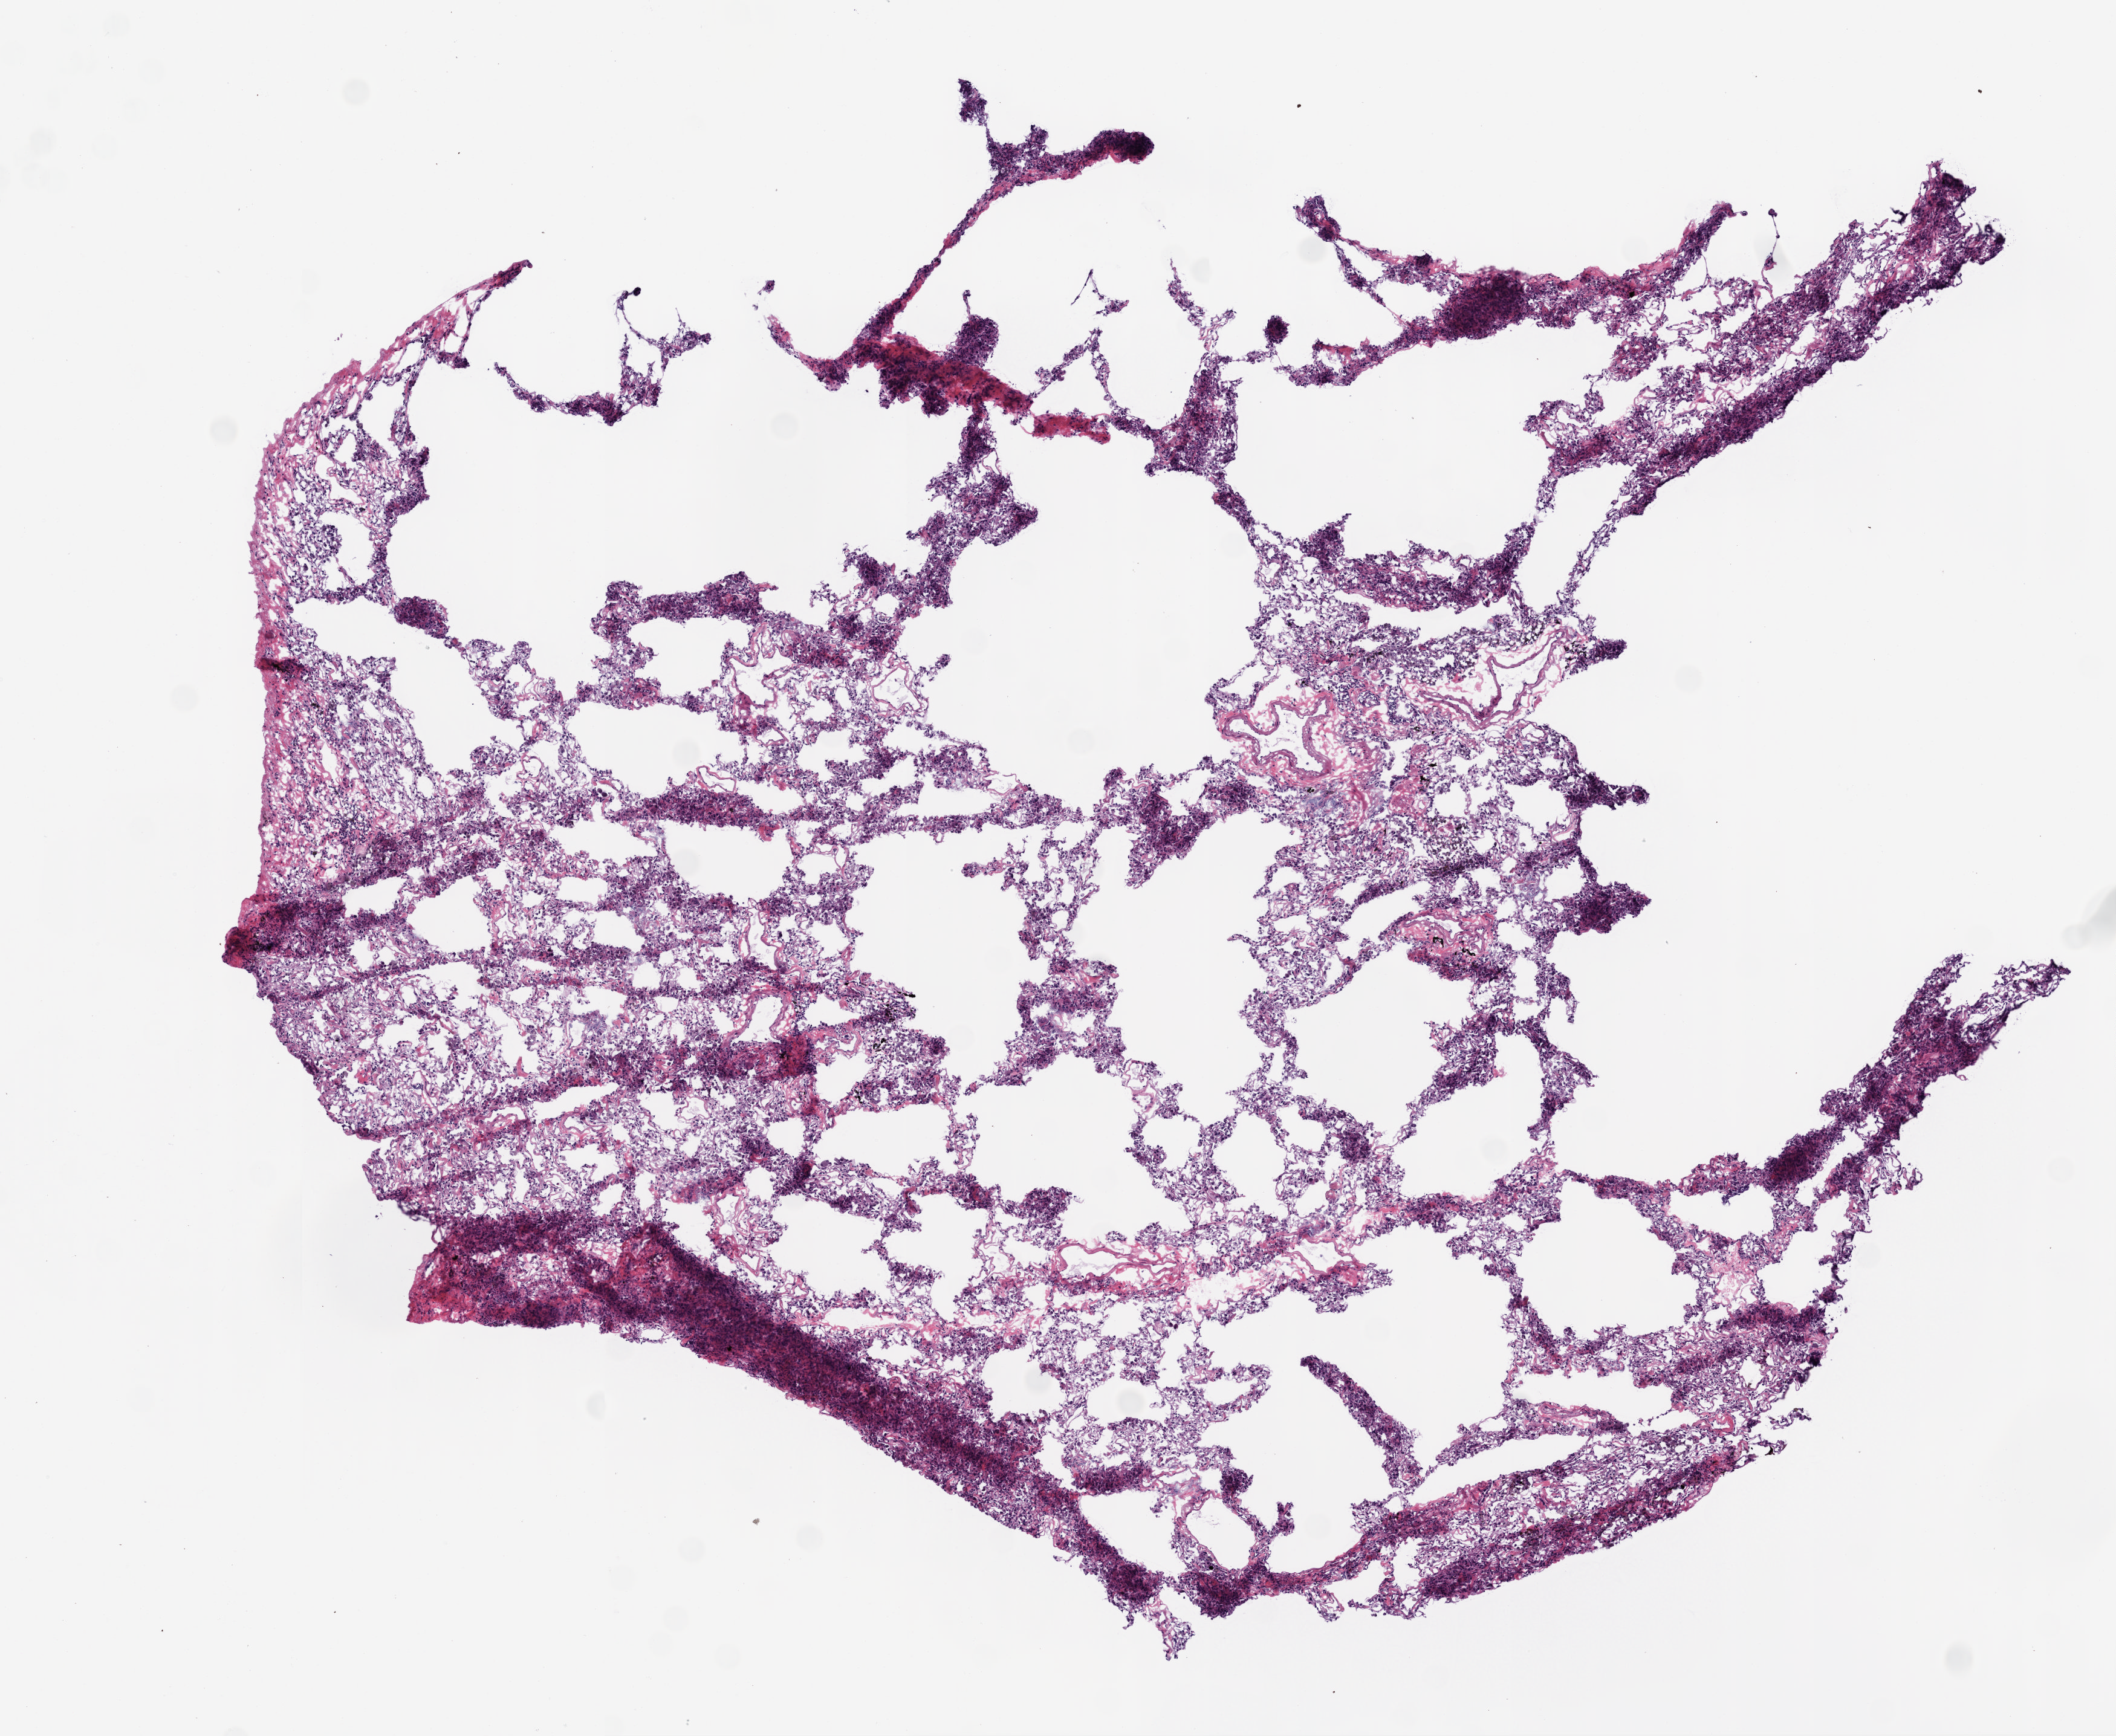
Digitized H&E tissue section (whole slide), shown as a low-resolution overview of the whole scanned area (about 7.0 x 5.8 mm, slide scanned at 20x). Frozen section from the top of the tissue portion. Lung, solid tissue normal (non-tumour tissue) sample. Patient: male, age at initial diagnosis 55 years.
This section: solid tissue normal sample (biorepository sample class). Patient diagnosis: Adenocarcinoma, NOS (upper lobe, lung).